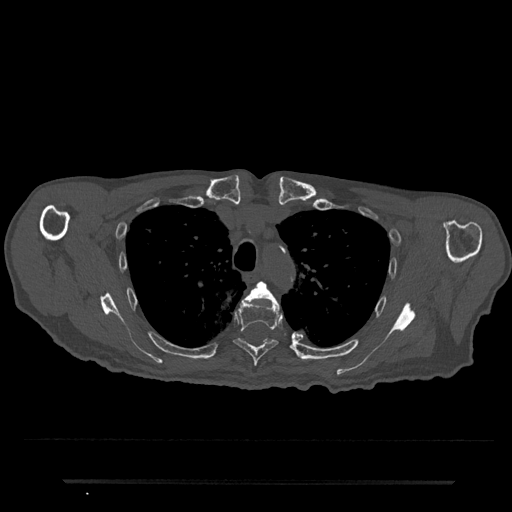
CT including the spine, one axial slice. Position 581 of 797 along the scan axis. Reconstruction kernel Br40s/3. Bone window (W 1800 / L 400 HU). 512 × 512 image matrix. Male patient, age 74 years. From the clinical record (not read from this slice): primary cancer: prostate.
Outlined on this slice (semi-automatic segmentation, software-assisted and operator-edited):
- T4 vertebra: bounding box <246,281,276,301> (left, top, right, bottom; pixels)
- T5 vertebra: <233,298,282,367>
- T6 vertebra: <264,338,268,343>